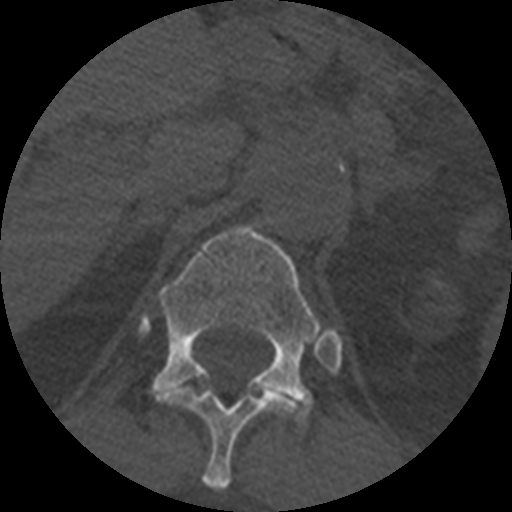
CT including the spine, one axial slice; slice 395 of 399 in the series (ordered by position); bone window (W 1800 / L 400 HU); 1.25 mm slice thickness; 512 × 512 image matrix, field of view 160 × 160 mm. Patient age 71 years. From the clinical record (not read from this slice): primary cancer: prostate.
Outlined on this slice (semi-automatic segmentation, software-assisted and operator-edited):
- T11 vertebra: box from (x=157, y=388) to (x=302, y=490) px
- T12 vertebra: (x=150, y=225)–(x=321, y=431)